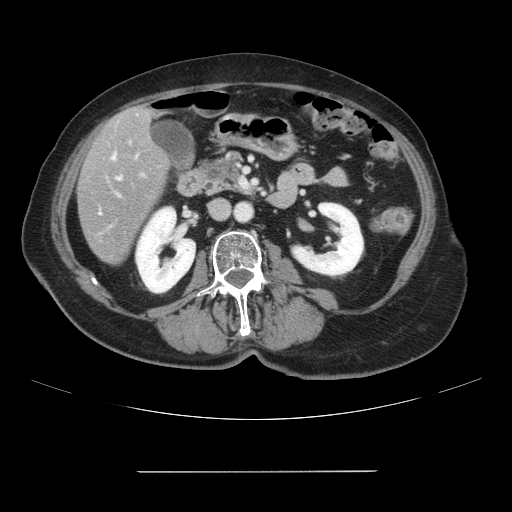
Contrast-enhanced abdominal CT, one axial slice; 120 kVp; intravenous contrast given; soft-tissue window (W 400 / L 40 HU); 2.5 mm slice thickness; 512 × 512 image matrix, field of view 400 × 400 mm. Female patient, age 74 years. From the clinical record (not read from this slice): diagnosis: colorectal cancer liver metastases, imaged before liver resection; multiple liver metastases: yes; largest metastasis: 1.1 cm; chemotherapy before resection: yes.
Annotated regions visible in this slice (expert manual segmentation):
- hepatic veins: box from (x=113, y=156) to (x=120, y=180) px
- liver: (x=78, y=107)–(x=170, y=264)
- planned liver remnant (the part of the liver to remain after resection): (x=144, y=109)–(x=152, y=118)